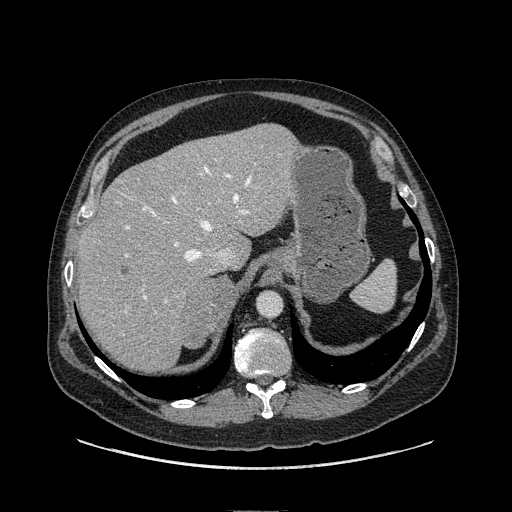
Contrast-enhanced abdominal CT, one axial slice; slice 84 of 149 in the series (ordered by position); soft-tissue window (W 400 / L 40 HU); 1.25 mm slice thickness; 512 × 512 image matrix, field of view 440 × 440 mm. Male patient. Case-level facts recorded for this patient, not image findings: diagnosis: adrenocortical carcinoma; tumour side: right adrenal; tumour size at pathology: 7.5 cm; Ki-67 index: 15 %; stage (as recorded): 2.
Structures marked on this image (semi-automatic segmentation, software-assisted and operator-edited):
- mass: box from (x=182, y=277) to (x=232, y=346) px